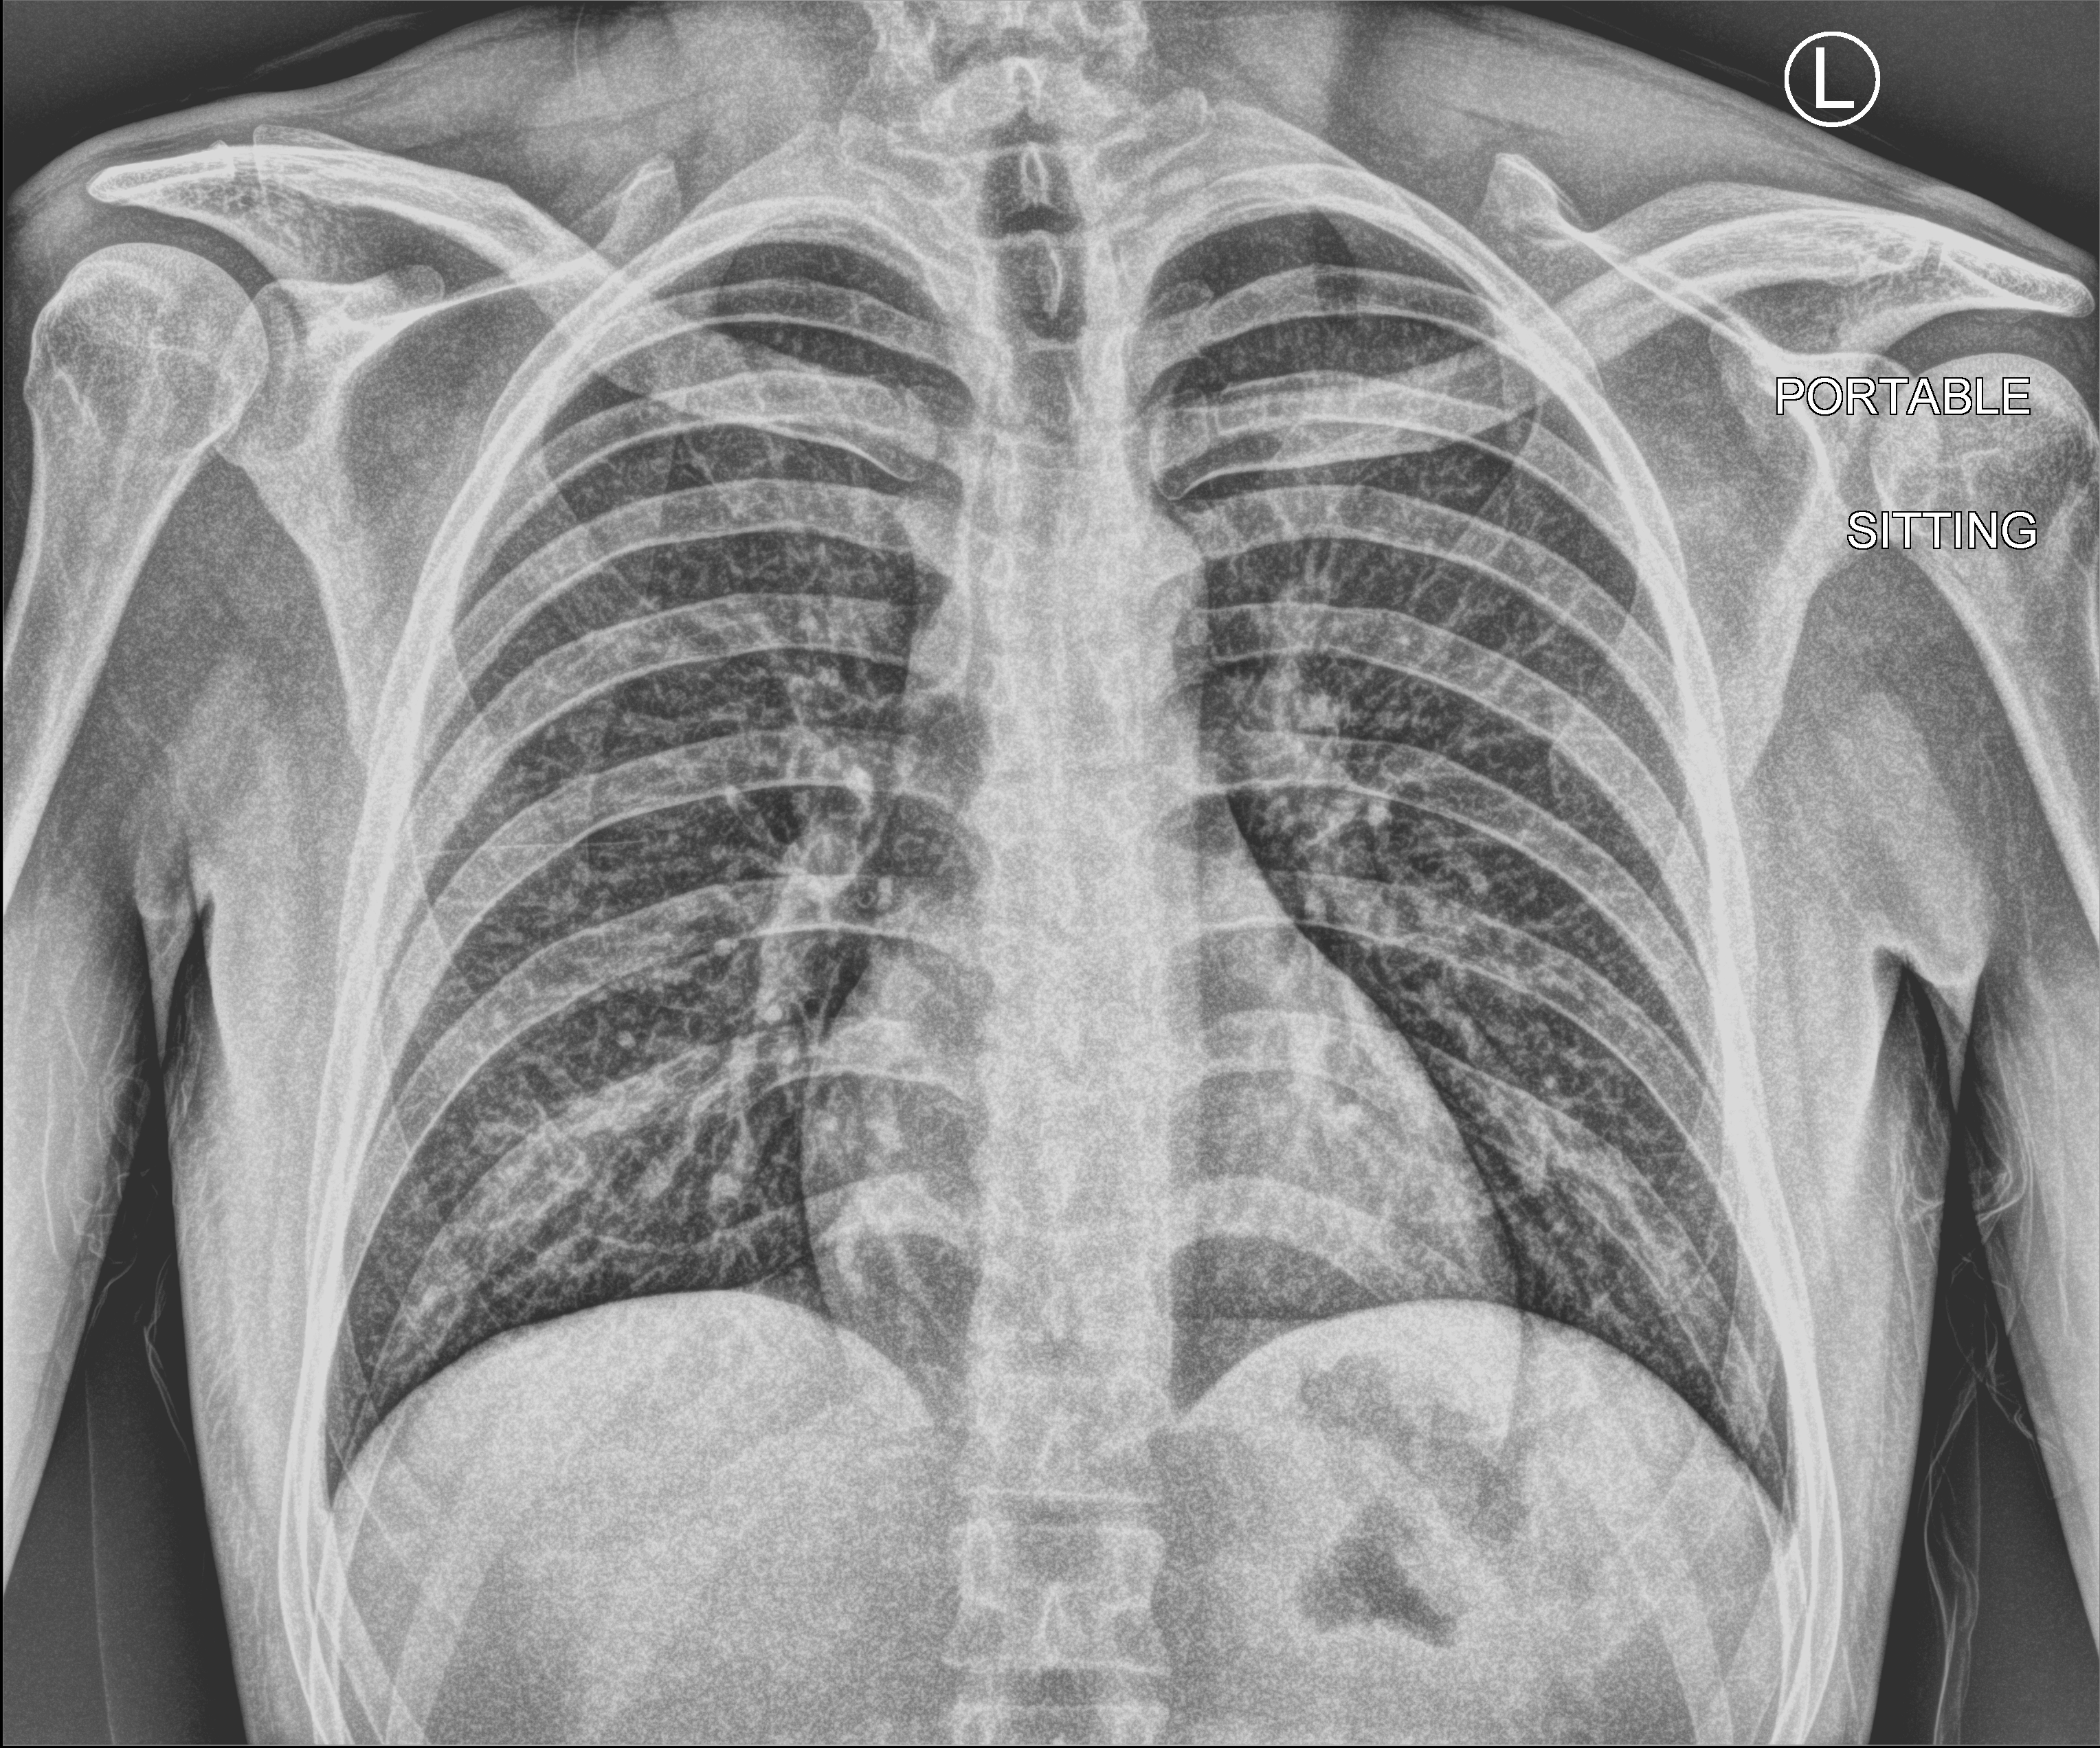
Bedside chest radiograph (computed radiography); anteroposterior (AP) projection. Patient hospitalised with COVID-19; male, aged 18–59 years.
Hospital-stay facts (about this admission, not read from this image; timing relative to this image not recorded): chronic kidney disease (admission record): no; diabetes (admission record): no.